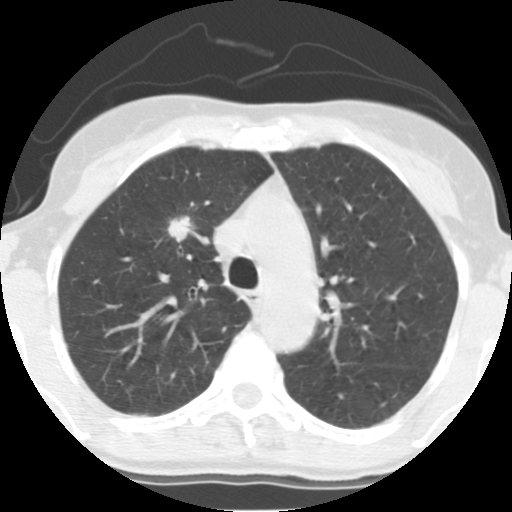
Low-dose screening chest CT, one axial slice; position 99 of 140 along the scan axis; reconstruction kernel STANDARD; 140 kVp; lung window (W 1500 / L -600 HU); 2.5 mm slice thickness; 512 × 512 image matrix, field of view 280 × 280 mm.
Structures marked on this image (outlined manually by an expert reader):
- lesion 1 (tumor, upper lobe of right lung): box from (x=166, y=215) to (x=191, y=243) px